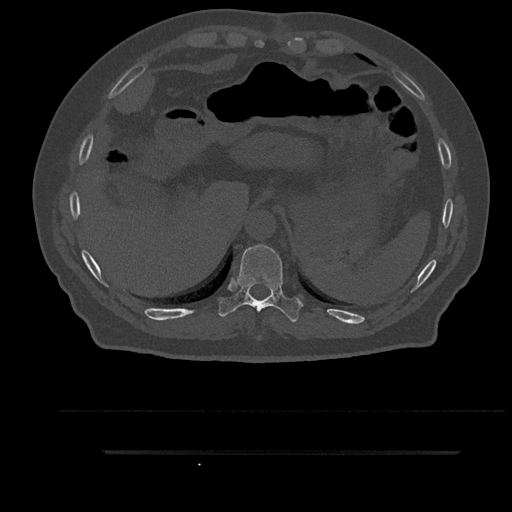
CT including the spine, one axial slice. Slice 373 of 797 in the series (ordered by position). Reconstruction kernel Br40s/3. Bone window (W 1800 / L 400 HU). 0.5 mm slice thickness. 512 × 512 image matrix. Male patient, age 63 years. Case-level facts recorded for this patient, not image findings: primary cancer: renal; vertebrae with lytic lesions (as recorded): T8.
Outlined on this slice (semi-automatic segmentation, software-assisted and operator-edited):
- T10 vertebra: bounding box <218,245,303,322> (left, top, right, bottom; pixels)